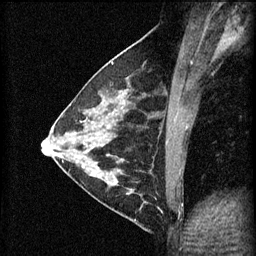
Breast MRI (dynamic contrast-enhanced), one sagittal slice; 3 images stored at this slice position (order not interpretable as contrast timing); 1.5 T; TE 4.2 ms, TR 11 ms; 256 × 256 image matrix, field of view 180 × 180 mm. Patient: female, 29 years.
Annotated regions visible in this slice (semi-automatically segmented with operator editing):
- analysis volume of interest (the breast-tissue region the enhancement analysis was run in; not a lesion): bounding box [x1, y1, x2, y2] px = [105, 172, 171, 227]
- tumour enhancement mask (voxels above the 70 % enhancement threshold inside the analysis volume of interest): [120, 172, 162, 211]